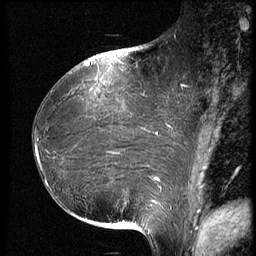
Breast MRI (dynamic contrast-enhanced), one sagittal slice. Slice 35 of 66 in the series (ordered by position). Dynamic contrast-enhanced series, image 2 of 3 at this slice position (ordered by acquisition). 1.5 T. TE 4.2 ms, TR 8.9 ms. 2.5 mm slice thickness. 256 × 256 image matrix, field of view 200 × 200 mm. Patient: female, 39 years. Case-level facts recorded for this patient, not image findings: setting: breast cancer imaged before/during neoadjuvant chemotherapy; receptor status: HER2-positive.
Structures marked on this image (semi-automatically segmented with operator editing):
- analysis volume of interest (the breast-tissue region the enhancement analysis was run in; not a lesion): box from (x=32, y=75) to (x=188, y=218) px
- tumour enhancement mask (voxels above the 140 % enhancement threshold inside the analysis volume of interest): (x=35, y=134)–(x=158, y=204)